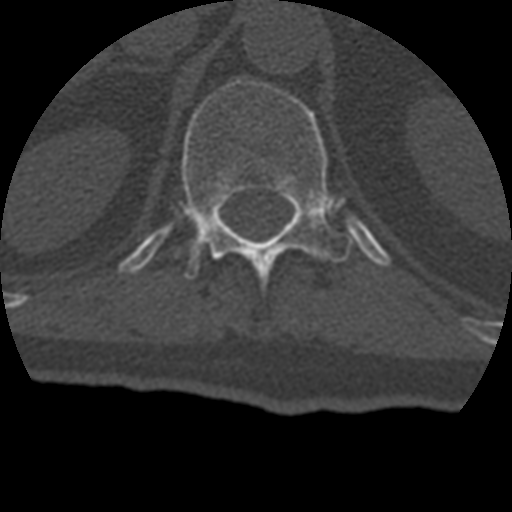
CT including the spine, one axial slice. Position 172 of 399 along the scan axis. Bone window (W 1800 / L 400 HU). 1.25 mm slice thickness. 512 × 512 image matrix, field of view 160 × 160 mm. Patient age 69 years. Case-level facts recorded for this patient, not image findings: primary cancer: prostate.
Structures marked on this image (semi-automatically segmented with operator editing):
- T12 vertebra: bounding box <182,79,352,281> (left, top, right, bottom; pixels)